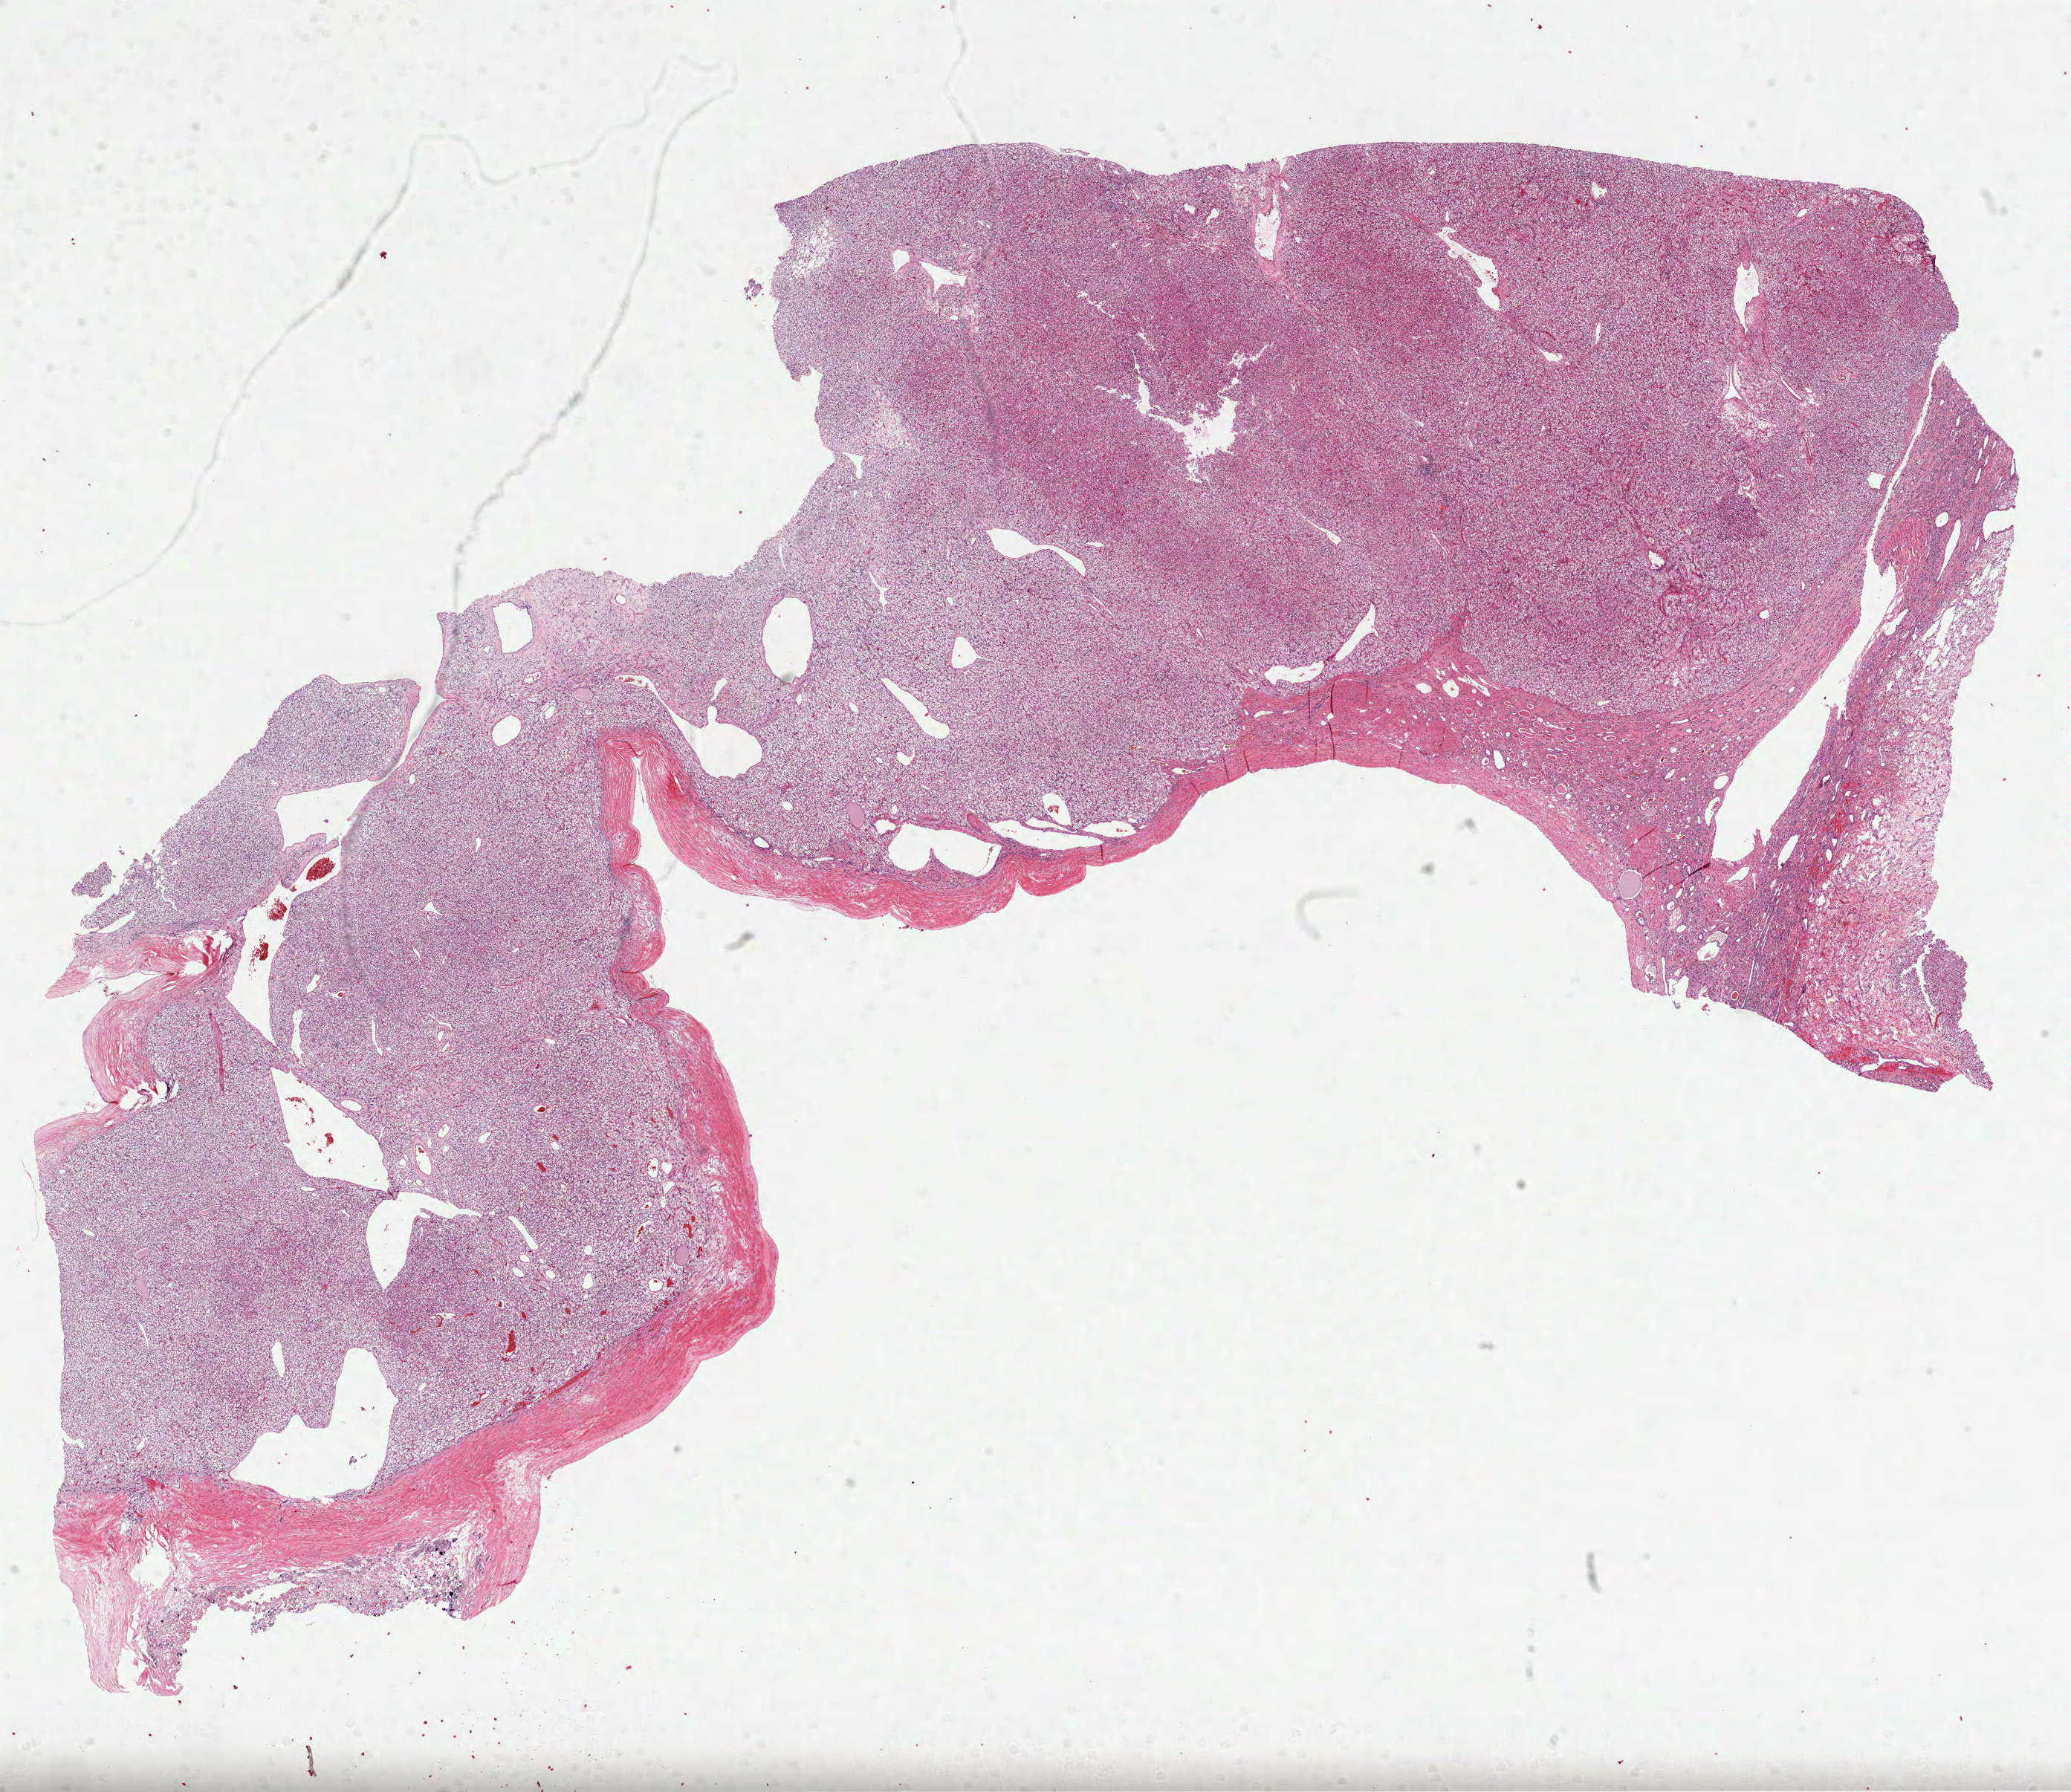
Digitized Hematoxylin and eosin (H&E) stained tissue section (whole slide) — shown as a low-resolution overview of the whole scanned area (about 22.5 x 19.5 mm, slide scanned at 40x); FFPE section; primary tumour sample from the kidney. Patient: female, age at initial diagnosis 76 years. Histologic grade: G3 (poorly differentiated).
Diagnosis: Clear cell adenocarcinoma, NOS. AJCC pathologic stage: III. TNM: T3a N0 M0. Laterality: left.